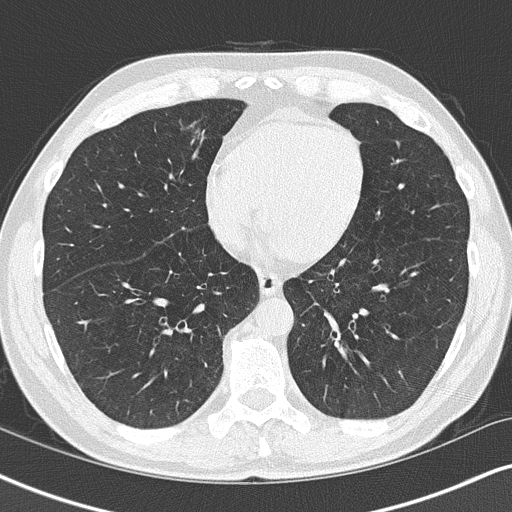
Low-dose screening chest CT, axial slice; second annual screen; lung window (W 1500 / L -600 HU); slice 107 of 148 in the series; 512 × 512 image matrix. Male, age 58 years at enrolment. Current smoker at enrolment.
Expert-annotated lung lesion, bounding box <167,107,226,157> (left, top, right, bottom; pixels). Screening reader's record for this exam (one nodule recorded; not confirmed to be the boxed lesion): non-calcified nodule or mass ≥4 mm, right middle lobe, 8 × 8 mm, spiculated (stellate) margins, soft tissue attenuation, pre-existing on the prior screen: yes; interval growth: yes. Official screen result: positive, other. Lung cancer was diagnosed 21 days after this screen: adenocarcinoma, NOS, right middle lobe, moderately differentiated (G2), stage IIA (AJCC 6th edition), 10 mm at pathology.